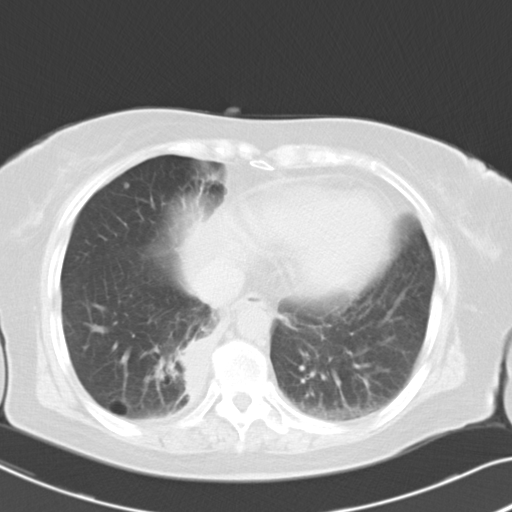
Chest CT, one axial slice. Position 8 of 26 along the scan axis. Reconstruction kernel B40f. 120 kVp. Lung window (W 1500 / L -600 HU). 512 × 512 image matrix. Patient: female, 70 years. From the clinical record (not read from this slice): clinical TNM (as recorded): T2 N1 M1a.
Annotated regions visible in this slice (rectangle marked by the reading radiologist):
- lung tumour (recorded histology: adenocarcinoma): bounding box (x1, y1, x2, y2) in pixels: (174, 326, 208, 406)